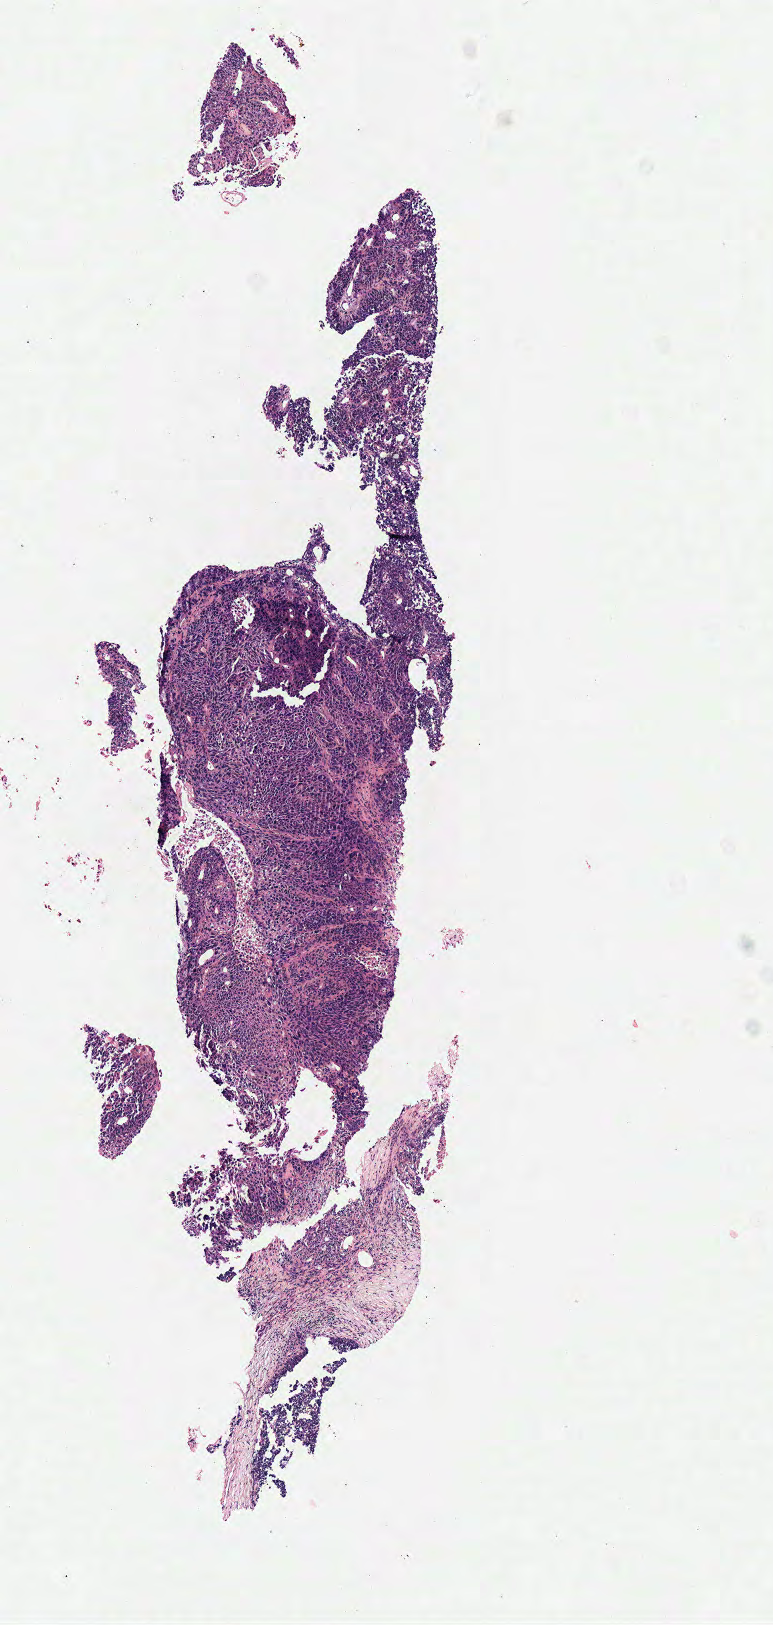
H&E whole-slide image — shown as a low-resolution overview of the whole scanned area (about 3.0 x 6.4 mm); frozen section; sample: primary tumour, lung. Male patient; age at initial diagnosis 74 years. Pathologist review of this section (percent, as recorded): tumour cells 85%, tumour nuclei 85%, normal cells 0%, stromal cells 15%, necrosis 0%.
- AJCC pathologic stage: IIA (6th edition)
- laterality: right
- pathologic diagnosis: Squamous cell carcinoma, NOS (upper lobe, lung)